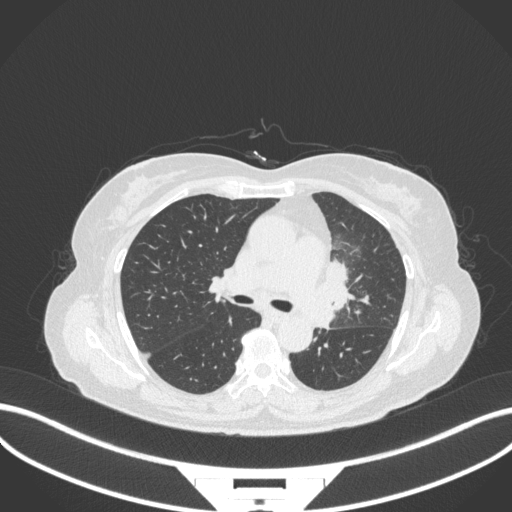
Chest CT, one axial slice. Position 204 of 382 along the scan axis. Lung window (W 1500 / L -600 HU). 1 mm slice thickness. 512 × 512 image matrix, field of view 400 × 400 mm. Female patient, age 64 years. Case-level facts recorded for this patient, not image findings: clinical TNM (as recorded): T2a N2 M0.
Structures marked on this image (bounding box drawn by a radiologist):
- lung tumour (recorded histology: adenocarcinoma): bounding box (x1, y1, x2, y2) in pixels: (313, 261, 356, 331)